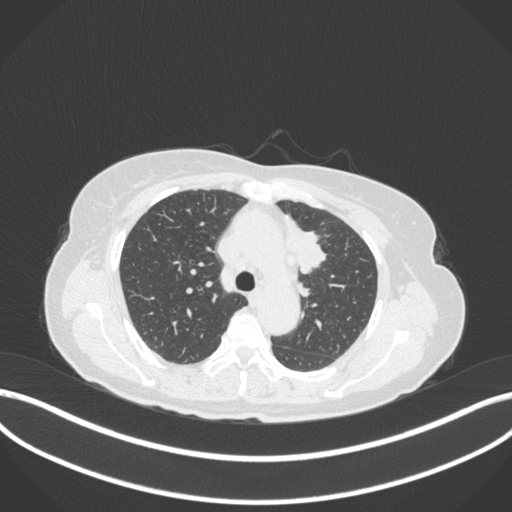
Chest CT, one axial slice; slice 236 of 368 in the series (ordered by position); reconstruction kernel B31f; 120 kVp; lung window (W 1500 / L -600 HU); 1 mm slice thickness; 512 × 512 image matrix. Patient: female, 65 years. From the clinical record (not read from this slice): clinical TNM (as recorded): T2a N0 M0; histopathological grade: G2-3.
Annotated regions visible in this slice (rectangle marked by the reading radiologist):
- lung tumour (recorded histology: adenocarcinoma): bounding box (x1, y1, x2, y2) in pixels: (280, 211, 330, 275)